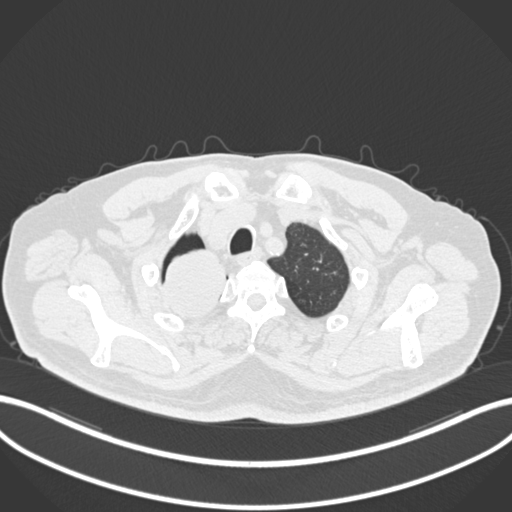
Chest CT, one axial slice. Slice 189 of 218 in the series (ordered by position). 120 kVp. Lung window (W 1500 / L -600 HU). 1 mm slice thickness. 512 × 512 image matrix, field of view 400 × 400 mm. Male patient, age 68 years. Case-level facts recorded for this patient, not image findings: clinical TNM (as recorded): T2a N0 M0.
Annotated regions visible in this slice (bounding box drawn by a radiologist):
- lung tumour (recorded histology: adenocarcinoma): bounding box [x1, y1, x2, y2] px = [162, 251, 229, 323]